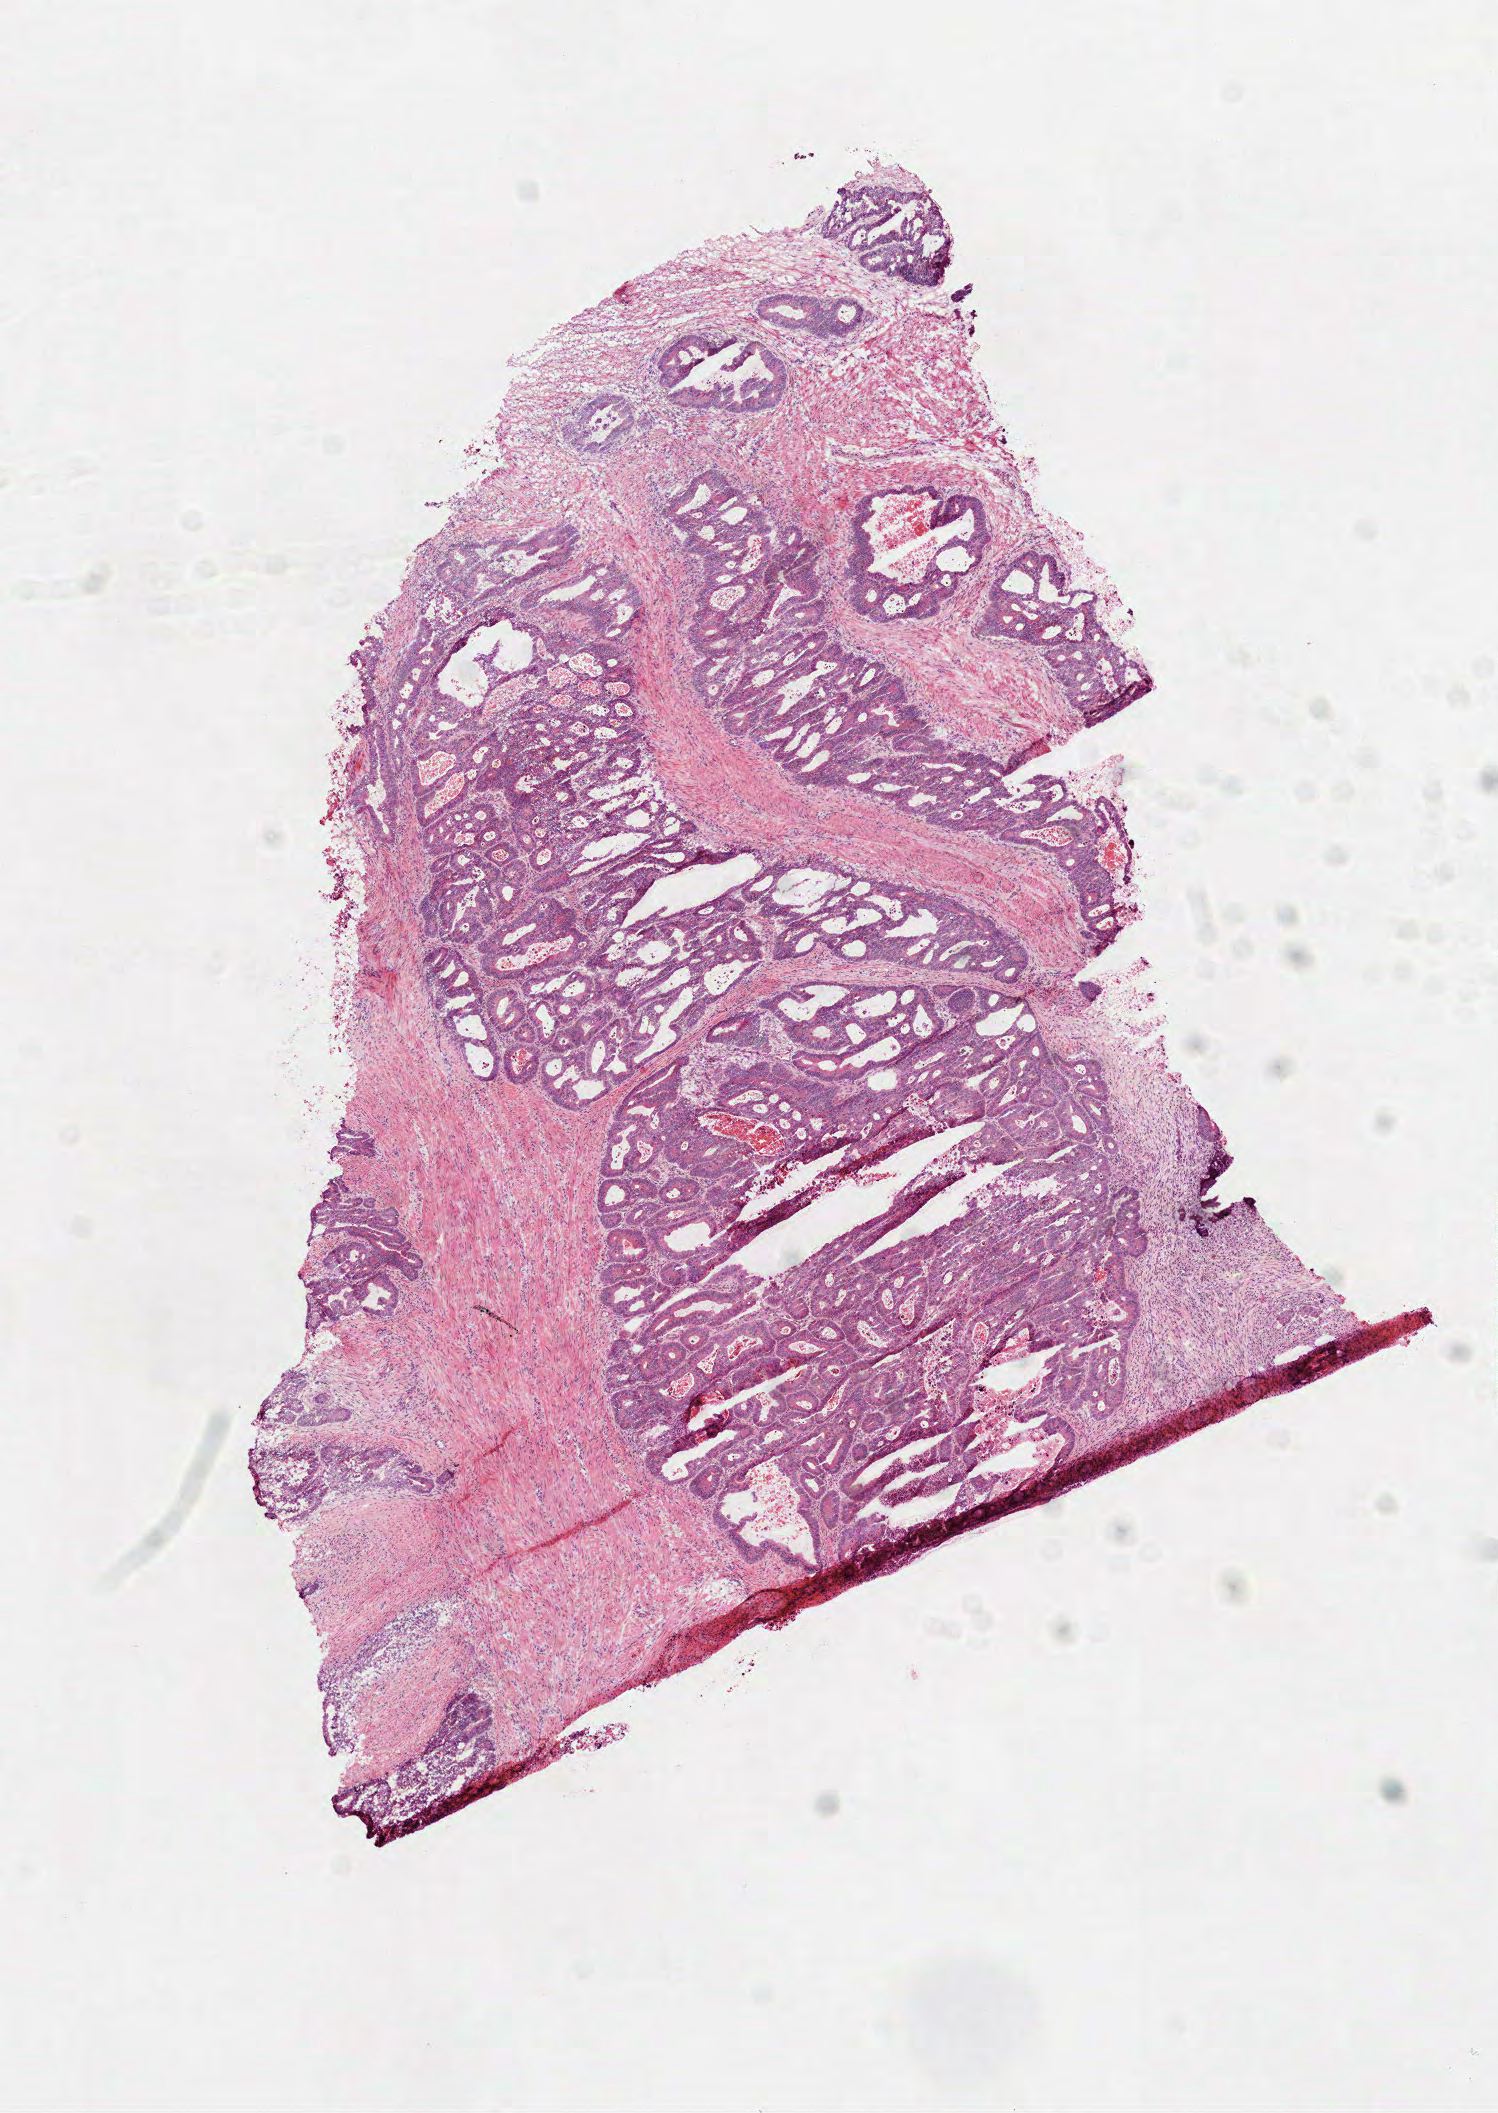
Digitized H&E tissue section (whole slide) — a low-resolution overview of the entire scanned area, about 6.0 x 8.5 mm (acquisition: 40x scan). Frozen section from the top of the tissue portion. Sample: primary tumour, rectum. Patient: female, age at initial diagnosis 59 years. Pathologist review of this section (percent, as recorded): tumour cells 52%, tumour nuclei 80%.
Diagnosis: Adenocarcinoma in tubulovillous adenoma.